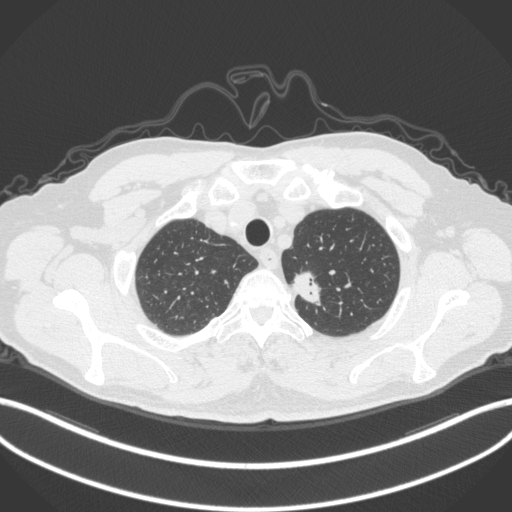
Chest CT, one axial slice; position 328 of 382 along the scan axis; 120 kVp; lung window (W 1500 / L -600 HU); 1 mm slice thickness; 512 × 512 image matrix. Patient: male, 64 years. Case-level facts recorded for this patient, not image findings: clinical TNM (as recorded): T1c N0 M0.
Outlined on this slice (bounding box drawn by a radiologist):
- lung tumour (recorded histology: adenocarcinoma): bounding box <290,265,328,308> (left, top, right, bottom; pixels)